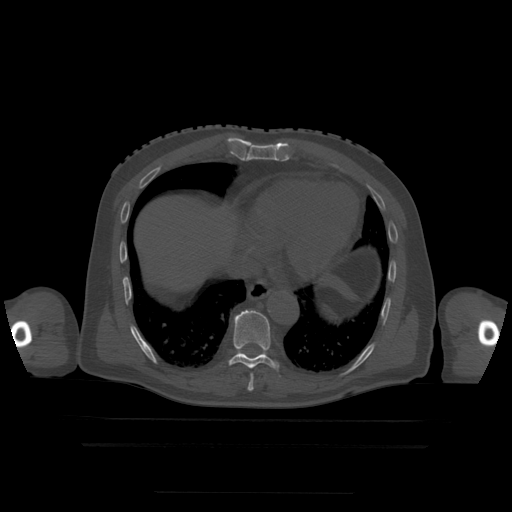
CT including the spine, one axial slice; position 261 of 522 along the scan axis; bone window (W 1800 / L 400 HU); 1.25 mm slice thickness; 512 × 512 image matrix, field of view 436 × 436 mm. Patient age 68 years. From the clinical record (not read from this slice): primary cancer: urothelial.
Annotated regions visible in this slice (semi-automatically segmented with operator editing):
- T7 vertebra: box from (x=248, y=385) to (x=254, y=392) px
- T8 vertebra: (x=249, y=375)–(x=254, y=386)
- T9 vertebra: (x=229, y=310)–(x=279, y=369)